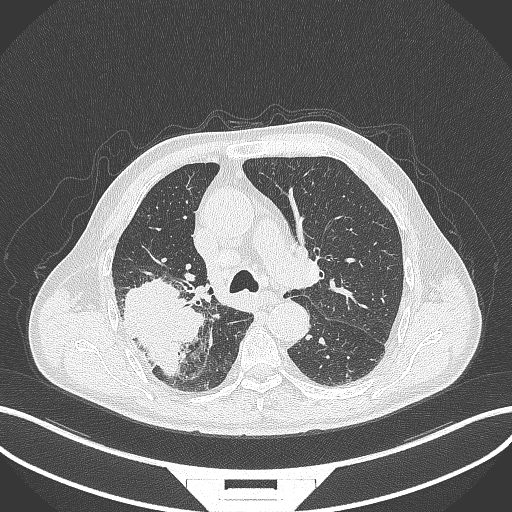
Chest CT, one axial slice. Position 270 of 429 along the scan axis. 120 kVp. Lung window (W 1500 / L -600 HU). 1 mm slice thickness. 512 × 512 image matrix, field of view 400 × 400 mm. Male patient, age 72 years. From the clinical record (not read from this slice): clinical TNM (as recorded): T3 N2 M0.
Annotated regions visible in this slice (rectangle marked by the reading radiologist):
- lung tumour (recorded histology: adenocarcinoma): box from (x=117, y=277) to (x=205, y=376) px